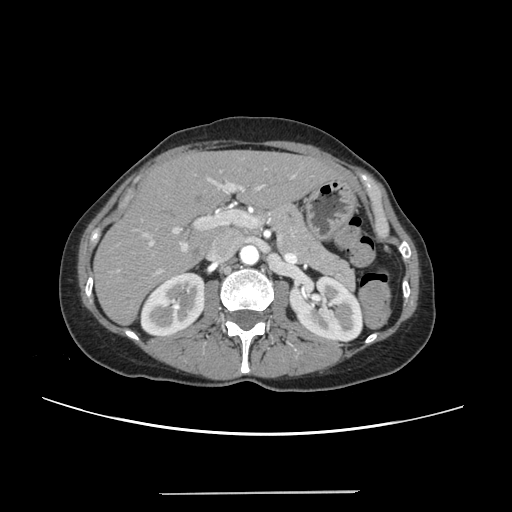
Contrast-enhanced abdominal CT, one axial slice. Position 137 of 240 along the scan axis. 120 kVp. Intravenous contrast given. Soft-tissue window (W 400 / L 40 HU). 1.25 mm slice thickness. 512 × 512 image matrix, field of view 371 × 371 mm. Female patient, age 60 years. Case-level facts recorded for this patient, not image findings: diagnosis: colorectal cancer liver metastases, imaged before liver resection; multiple liver metastases: no; largest metastasis: 1.5 cm; chemotherapy before resection: yes.
Structures marked on this image (manually delineated by an expert):
- liver: bounding box (x1, y1, x2, y2) in pixels: (95, 152, 340, 323)
- planned liver remnant (the part of the liver to remain after resection): (95, 152, 340, 323)
- portal vein (with intrahepatic branches): (116, 168, 296, 274)